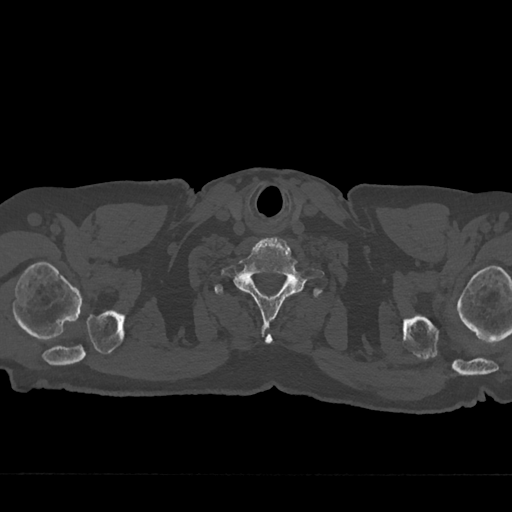
CT including the spine, one axial slice; slice 689 of 797 in the series (ordered by position); 120 kVp; bone window (W 1800 / L 400 HU); 0.5 mm slice thickness; 512 × 512 image matrix, field of view 377 × 377 mm. Male patient, age 75 years. Case-level facts recorded for this patient, not image findings: primary cancer: renal.
Outlined on this slice (semi-automatic segmentation, software-assisted and operator-edited):
- T1 vertebra: bounding box [x1, y1, x2, y2] px = [215, 283, 301, 294]